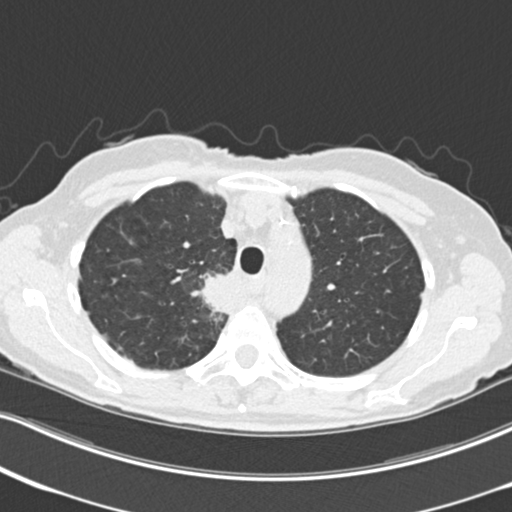
Chest CT (low-dose screening protocol), one axial image; third annual screen; lung window (W 1500 / L -600 HU); standard (soft-tissue) reconstruction kernel (B30f); slice 54 of 226 in the series. Female participant, aged 68 years at enrolment.
Lesion marked by an expert reader, bounding box (x1, y1, x2, y2) in pixels: (197, 266, 249, 322). Reader record for this screening exam (exam-level; its link to the box is not recorded): non-calcified nodule or mass ≥4 mm, right upper lobe, 31 × 29 mm, poorly defined margins, soft tissue attenuation, pre-existing on the prior screen: no. Later outcome: lung cancer diagnosed 79 days after this screen — squamous cell carcinoma, NOS, right upper lobe, mediastinum, poorly differentiated (G3), stage IIIB (AJCC 6th edition), 43 mm at pathology.